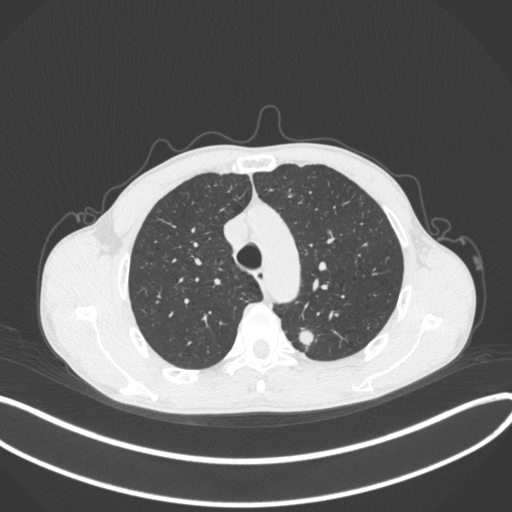
Chest CT, one axial slice; slice 300 of 429 in the series (ordered by position); 120 kVp; lung window (W 1500 / L -600 HU); 1 mm slice thickness; 512 × 512 image matrix, field of view 400 × 400 mm. Patient: male, 51 years. Case-level facts recorded for this patient, not image findings: clinical TNM (as recorded): T2a N1 M1.
Annotated regions visible in this slice (rectangle marked by the reading radiologist):
- lung tumour (recorded histology: adenocarcinoma): box from (x=294, y=323) to (x=319, y=350) px